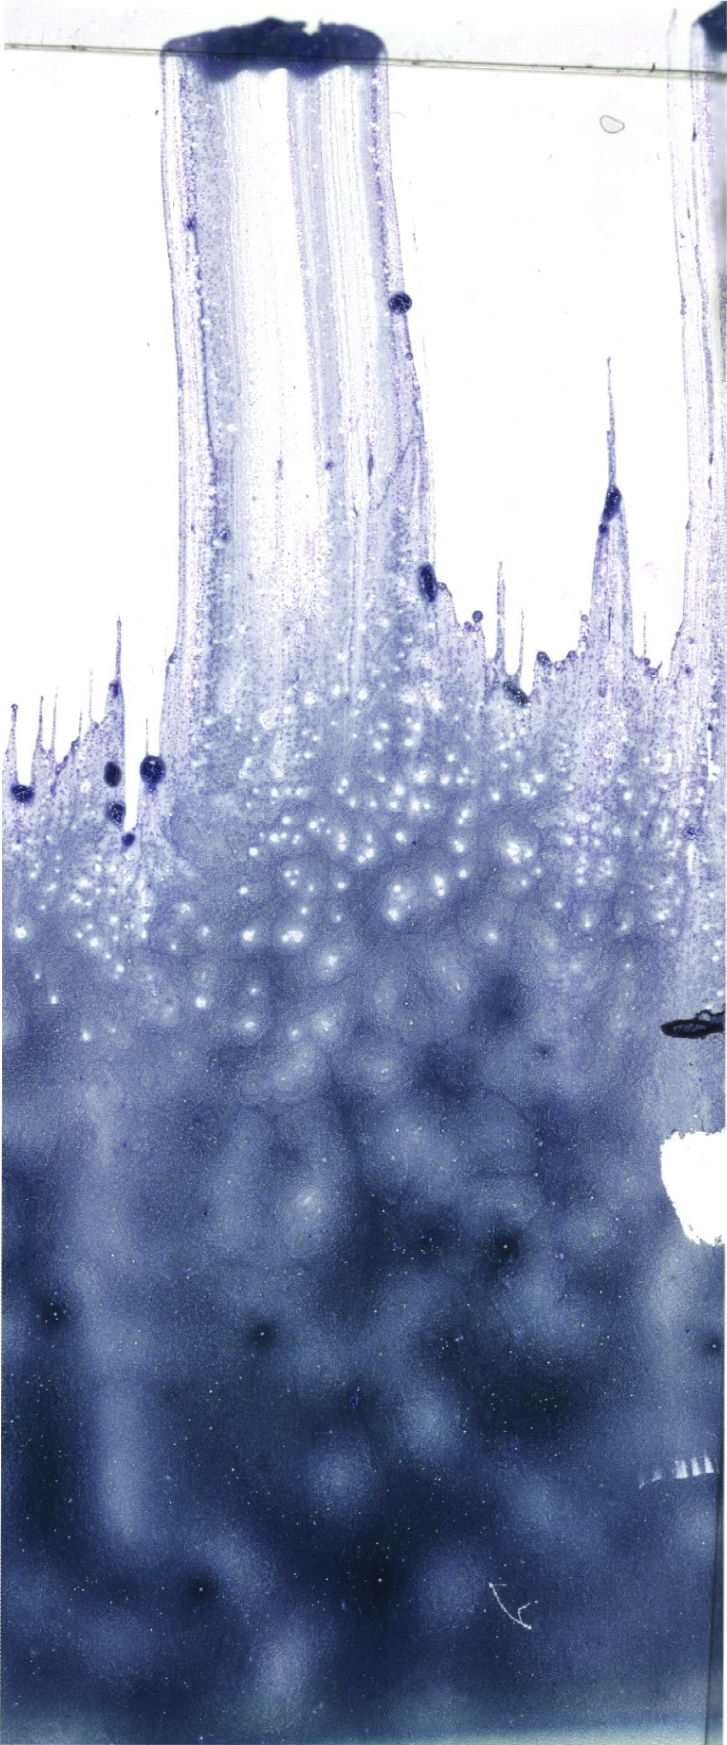
Whole-slide image of a May-Grünwald–Giemsa-stained bone marrow aspirate smear, a low-resolution overview of the entire scanned area, about 20.6 x 49.5 mm.
Diagnosis: Burkitt Leukemia.